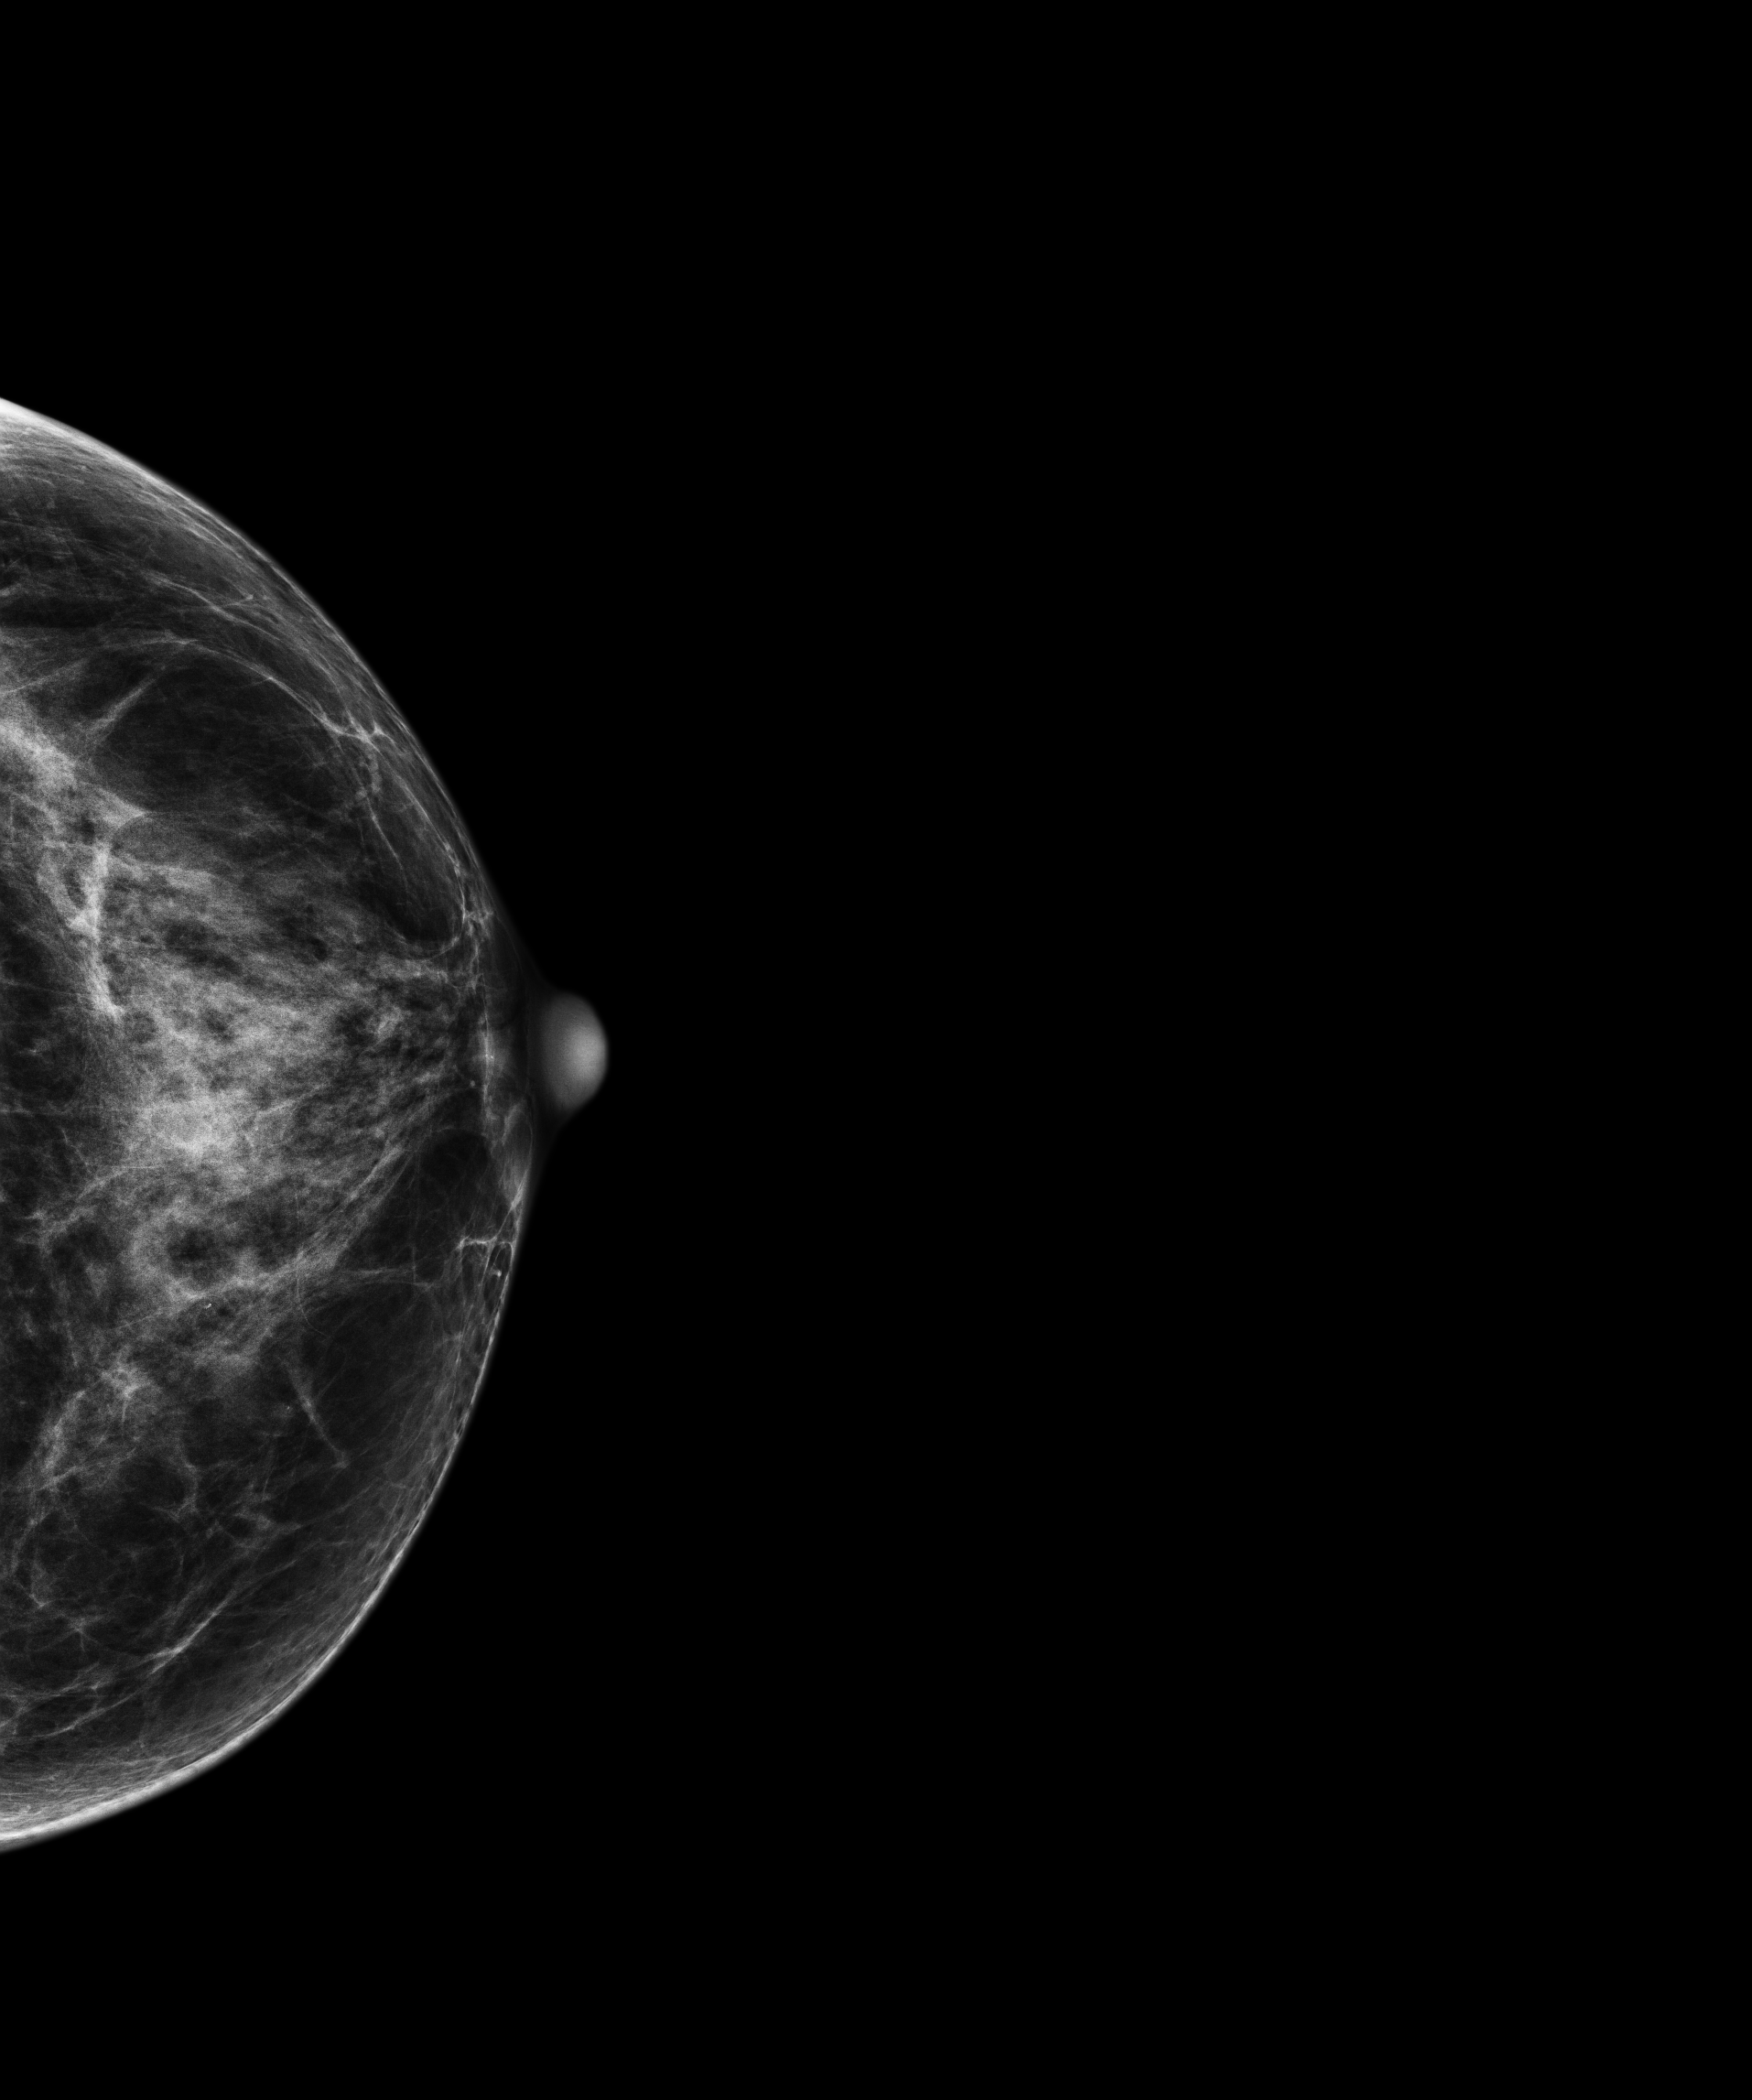
Annual screening mammography examination; compressed breast thickness 57.3 mm. Patient: female, 65 years.
Image type: full-field digital mammogram. Breast: left. Projection: CC view.